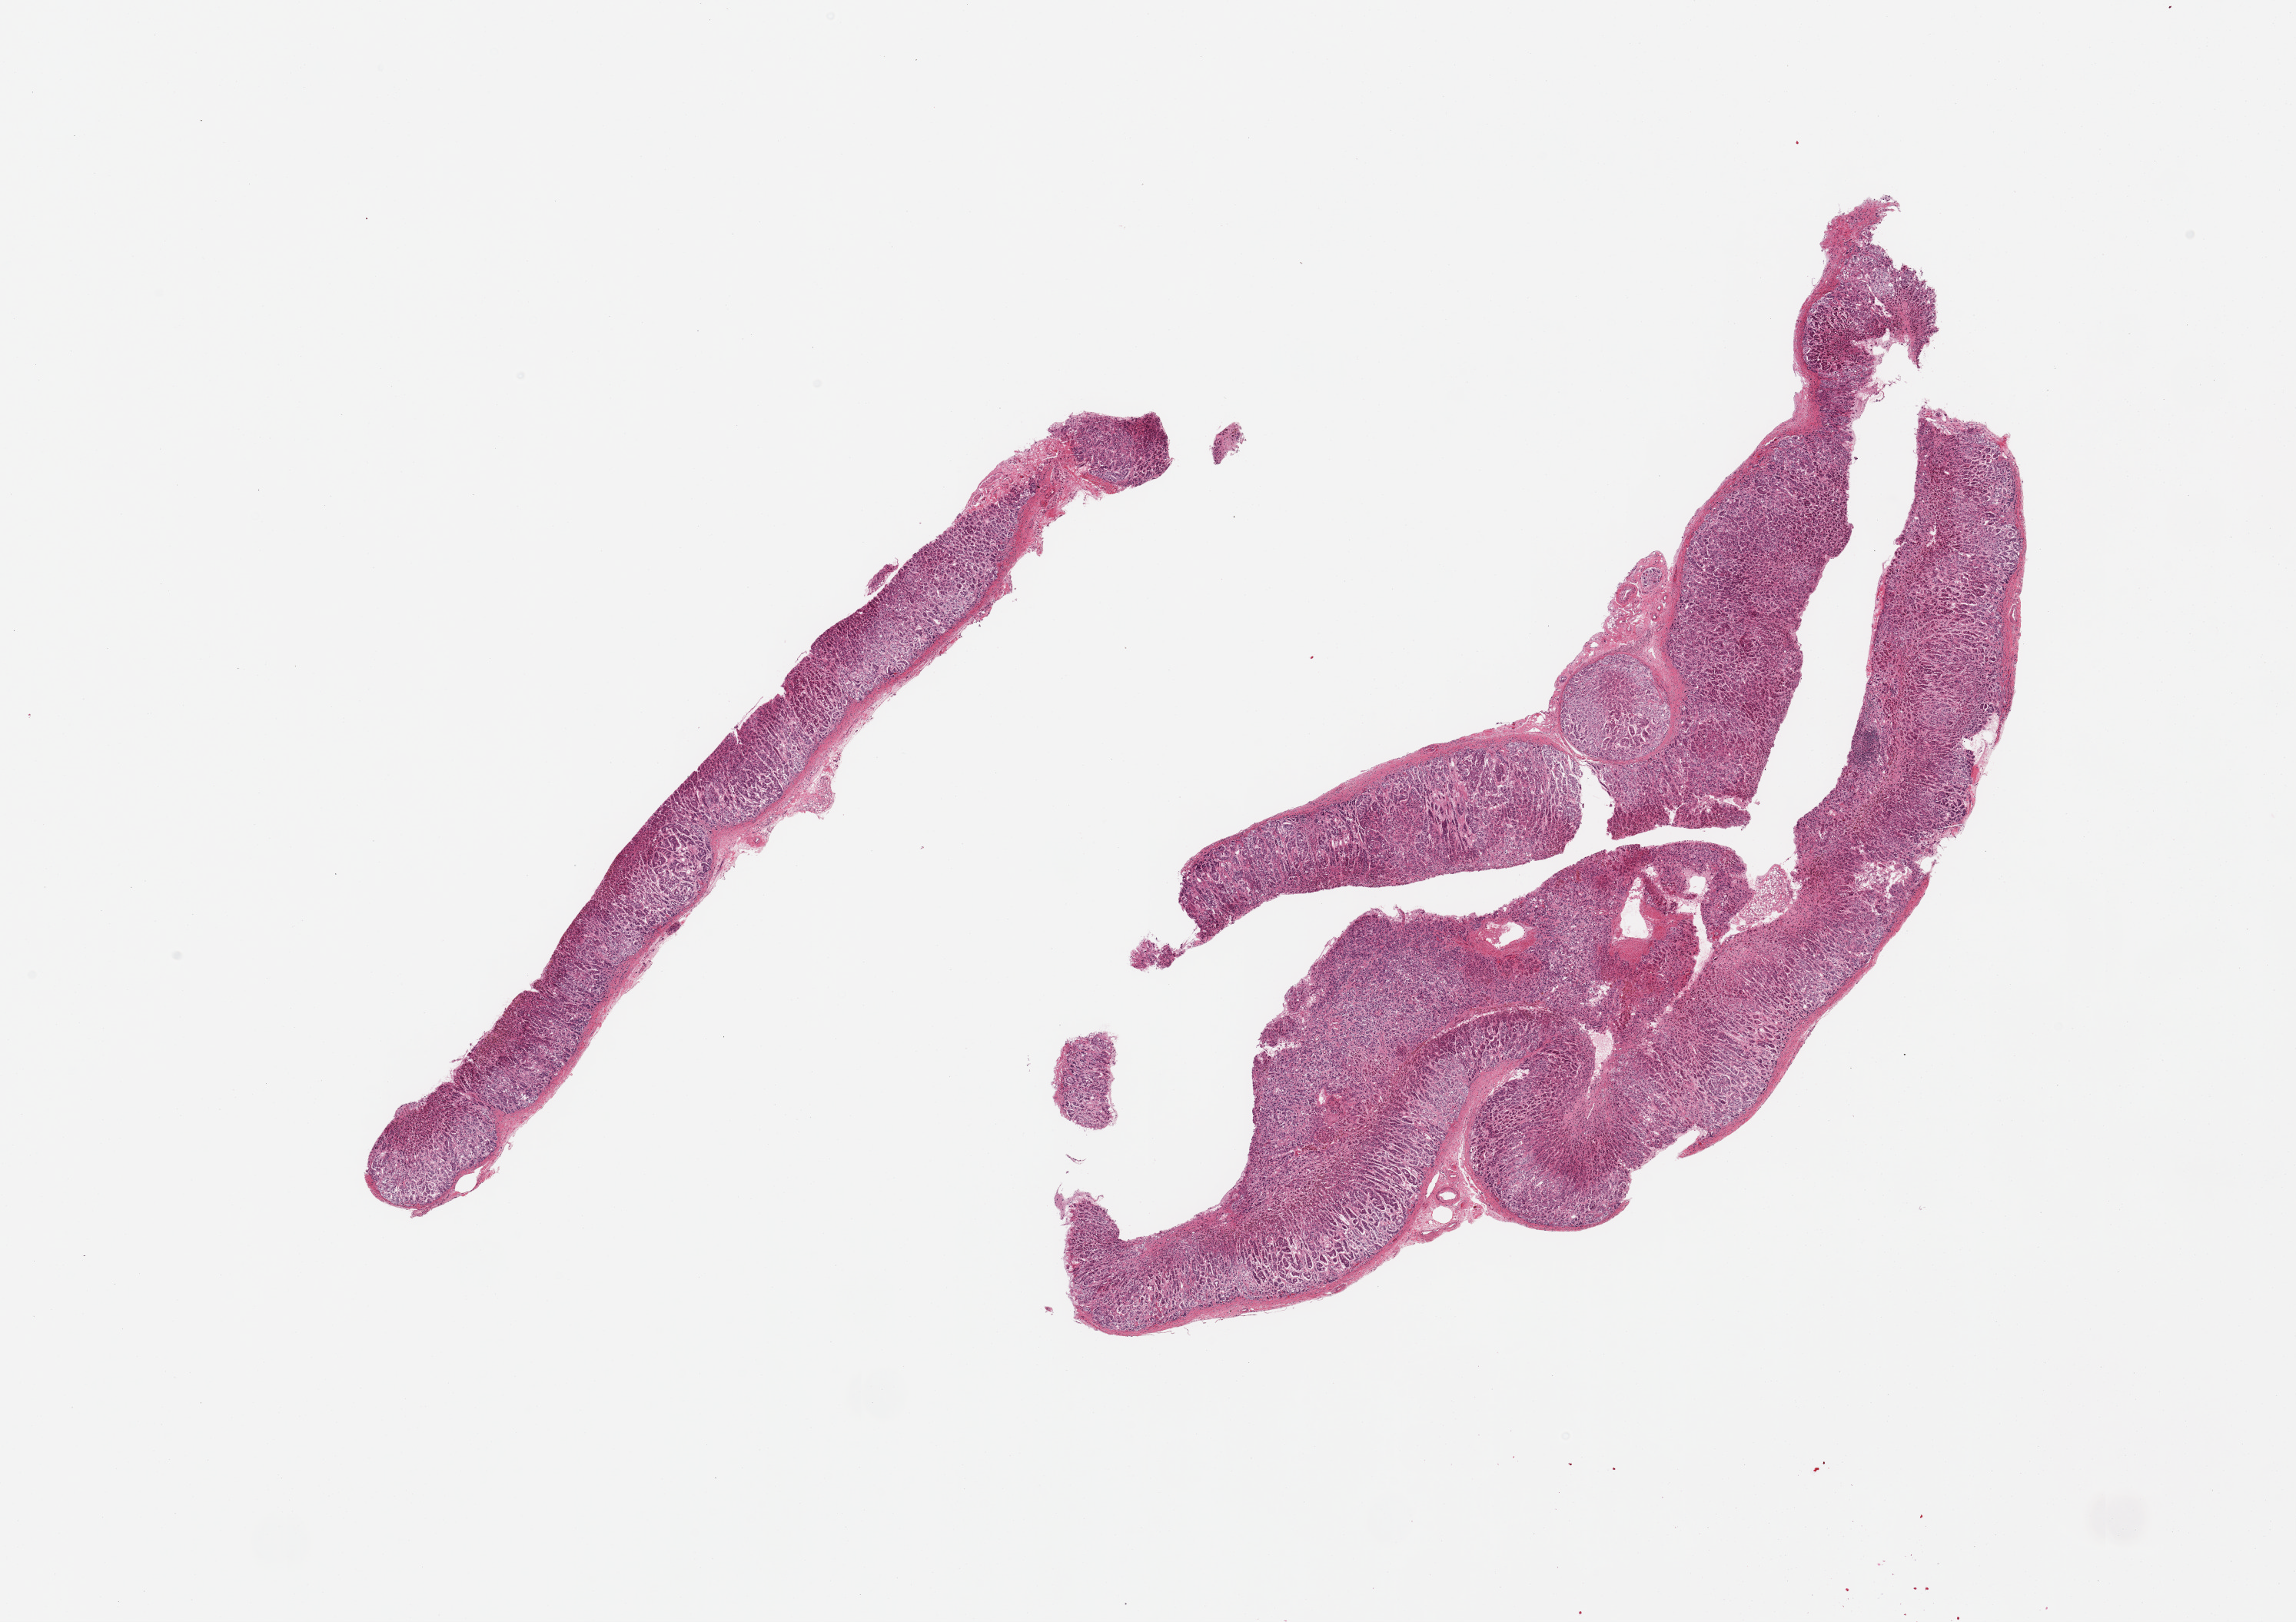
Digitized H&E-stained section, whole scanned area (about 23.6 x 16.7 mm) shown as a low-resolution overview, PAXgene-fixed paraffin-embedded (PFPE) section, section of adrenal gland (target tissue), tissue donor sample. Donor: male.
Review note (as recorded): 2 pieces; well dissected.